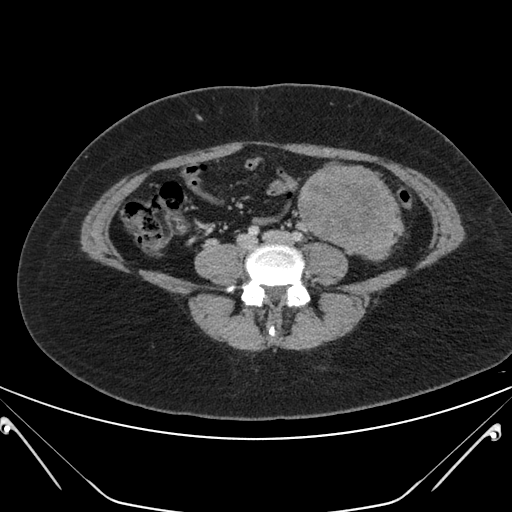
Contrast-enhanced abdominal CT, one axial slice; position 72 of 168 along the scan axis; intravenous contrast given; soft-tissue window (W 400 / L 40 HU); 512 × 512 image matrix, field of view 394 × 394 mm. Patient: female, 26 years. Case-level facts recorded for this patient, not image findings: diagnosis: adrenocortical carcinoma; tumour side: left adrenal; tumour size at pathology: 28 cm; Ki-67 index: 20 %; stage (as recorded): 2.
Annotated regions visible in this slice (semi-automatic segmentation, software-assisted and operator-edited):
- mass: bounding box [x1, y1, x2, y2] px = [300, 167, 395, 258]